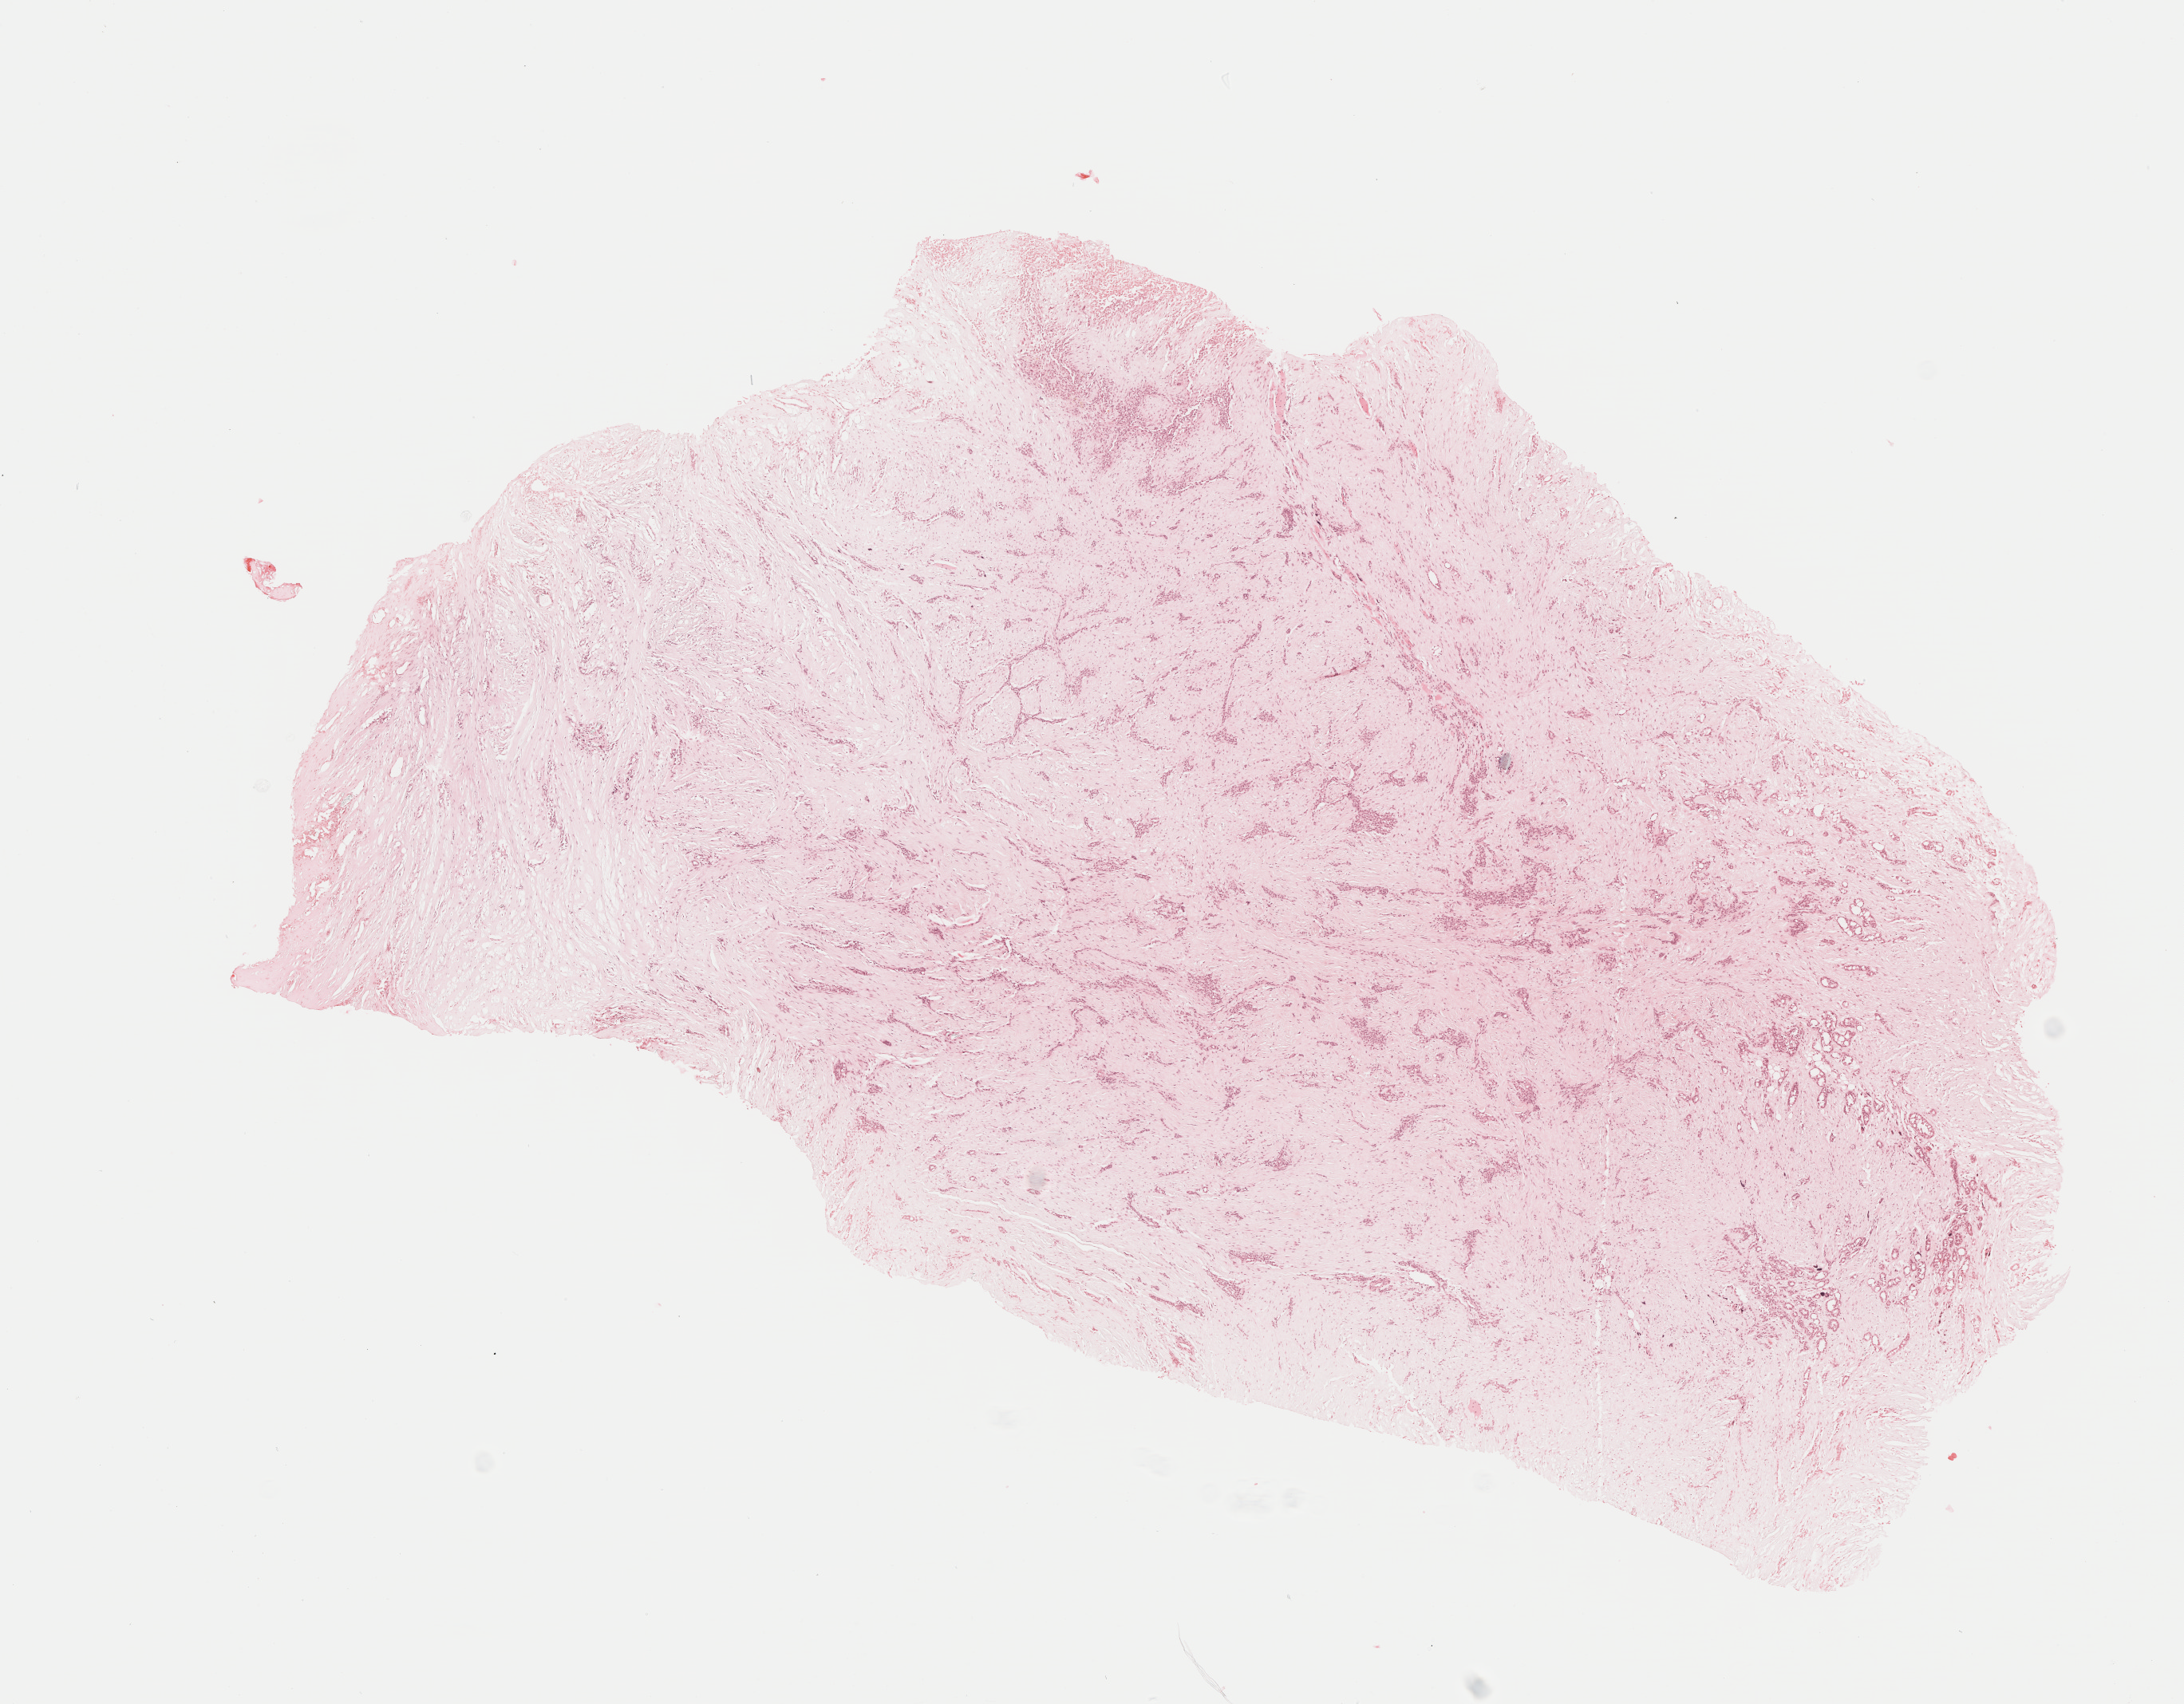
Digitized Hematoxylin and eosin (H&E) stained tissue section (whole slide), shown as a low-resolution overview of the whole scanned area (about 10.8 x 8.4 mm). Formalin-fixed paraffin-embedded (FFPE) diagnostic section. Mesothelium, primary tumour sample. Patient: male, age at initial diagnosis 50 years.
• AJCC pathologic stage: III
• laterality: right
• histologic diagnosis: Epithelioid mesothelioma, malignant (pleura, NOS)